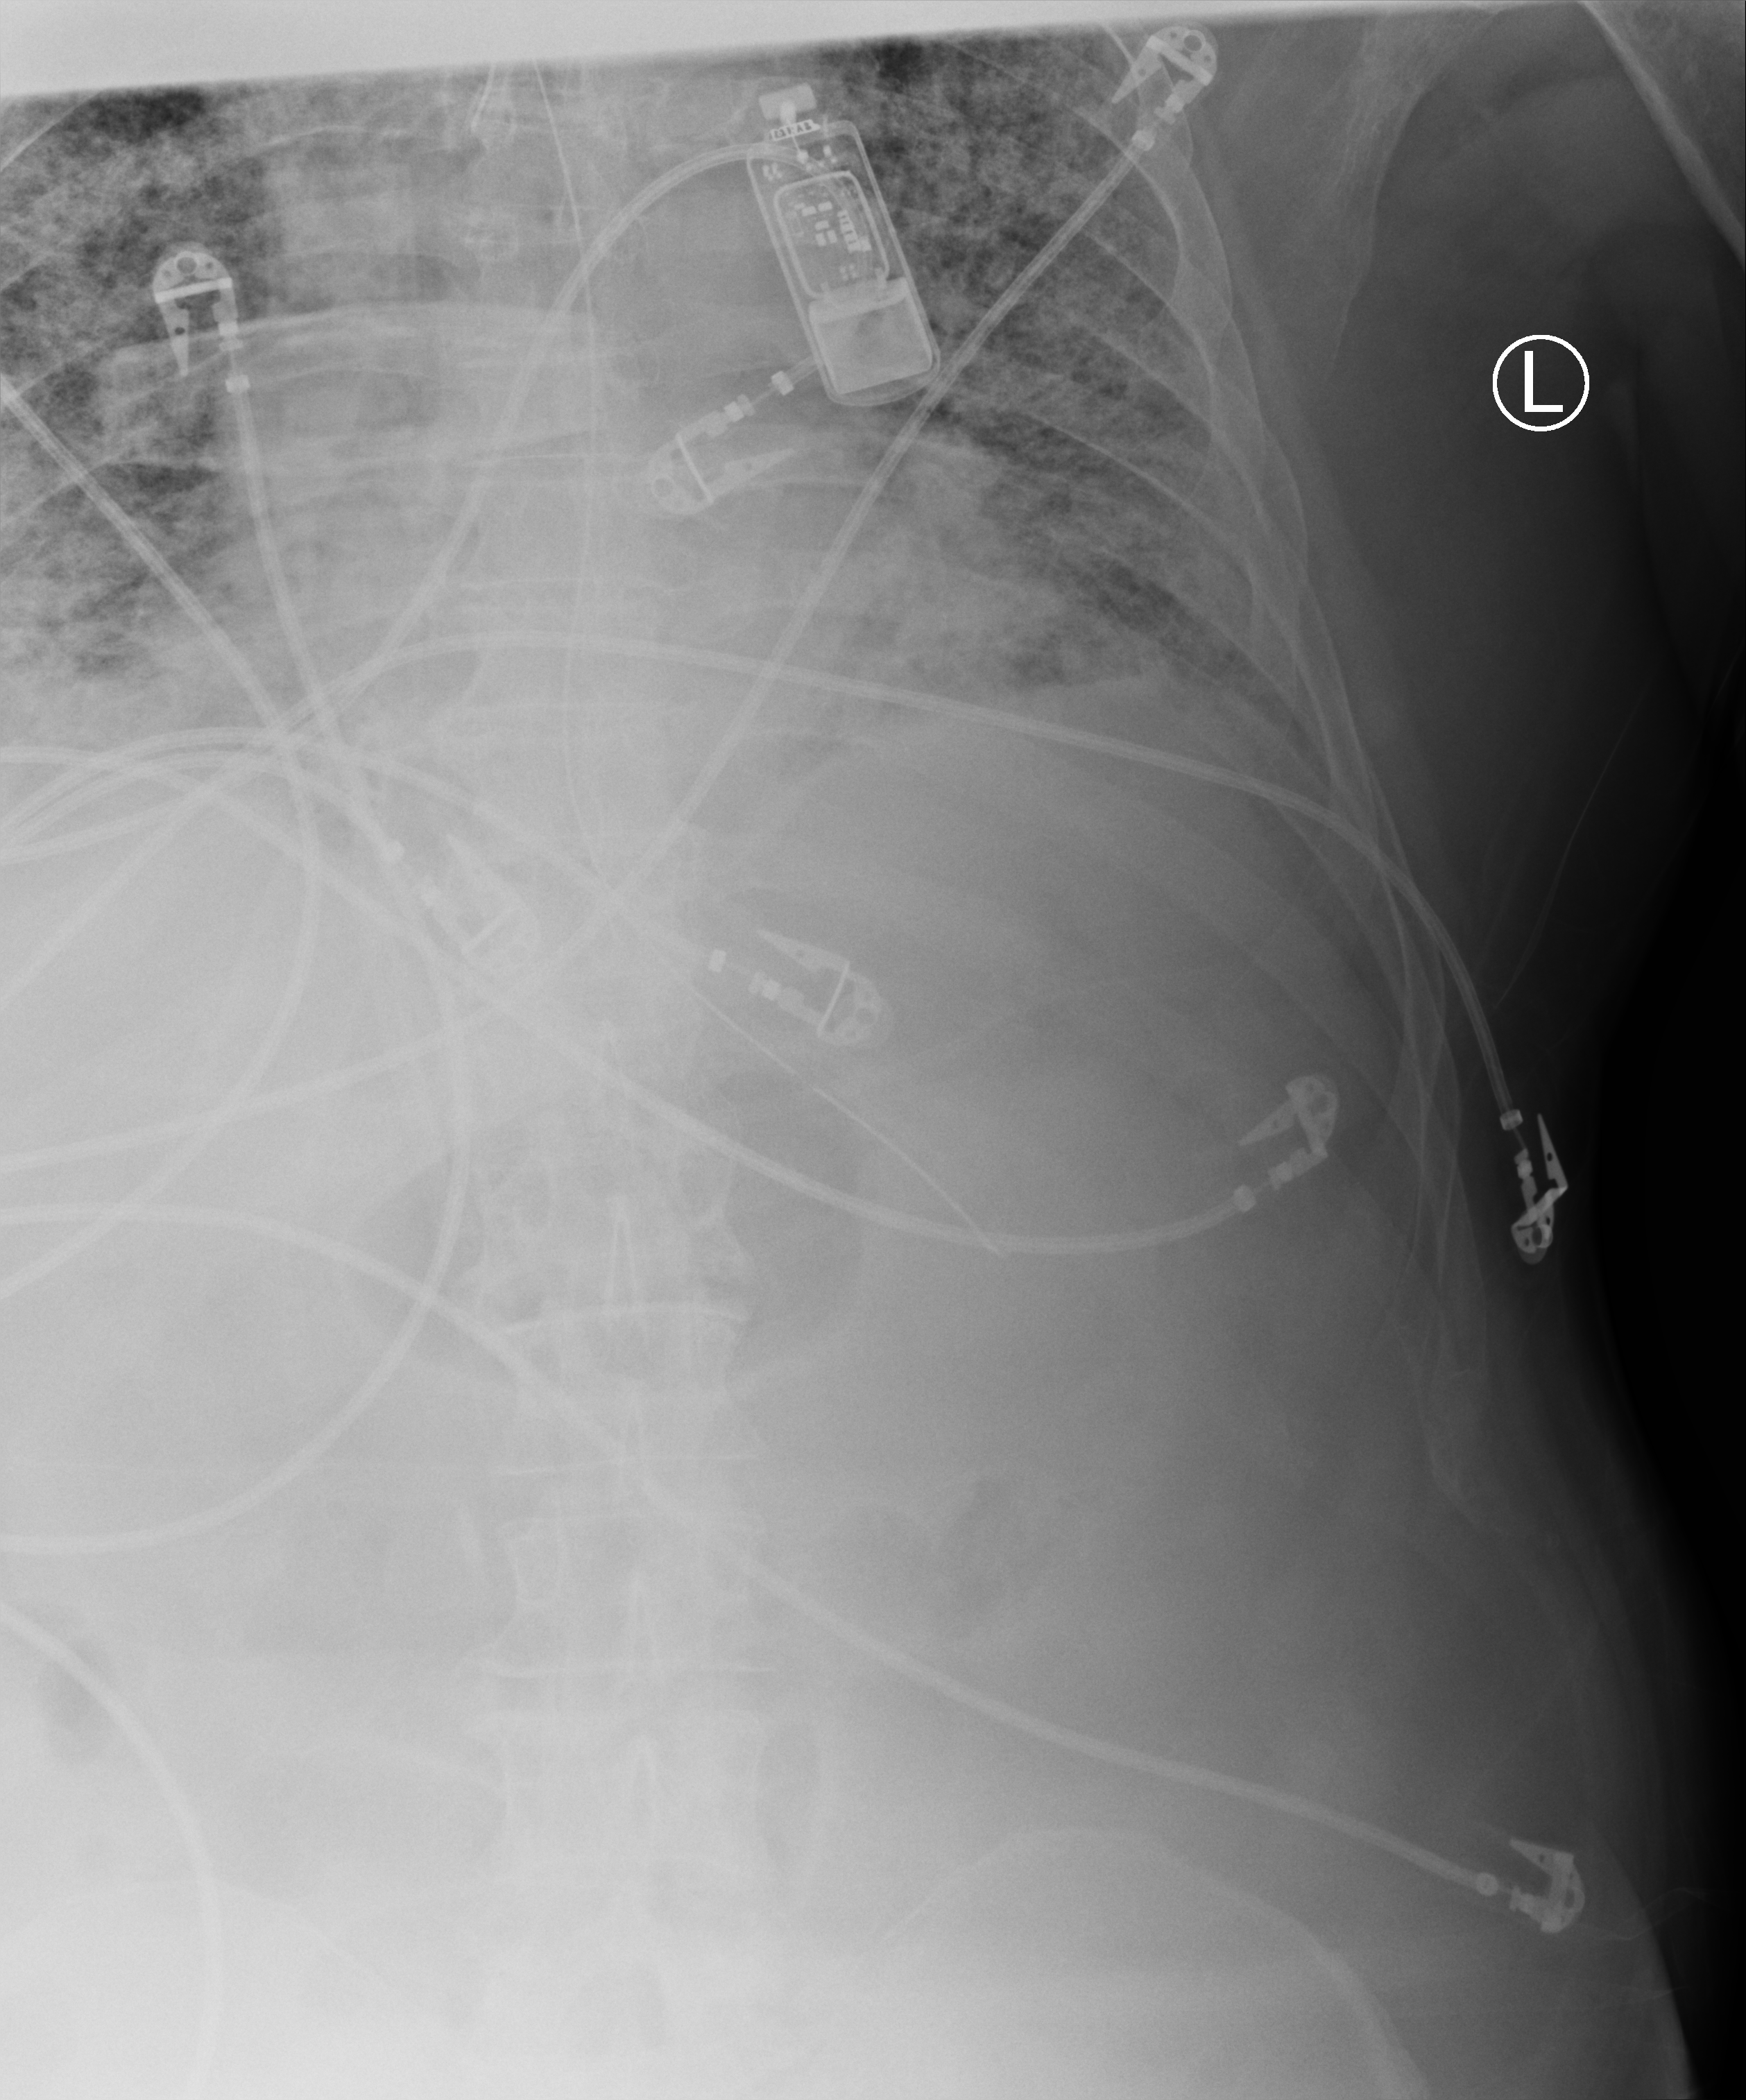
Portable chest radiograph; anteroposterior (AP) projection. Patient hospitalised with COVID-19; male, aged 60–74 years.
Hospital-stay facts (about this admission, not read from this image; timing relative to this image not recorded):
- other chronic lung disease (admission record): yes